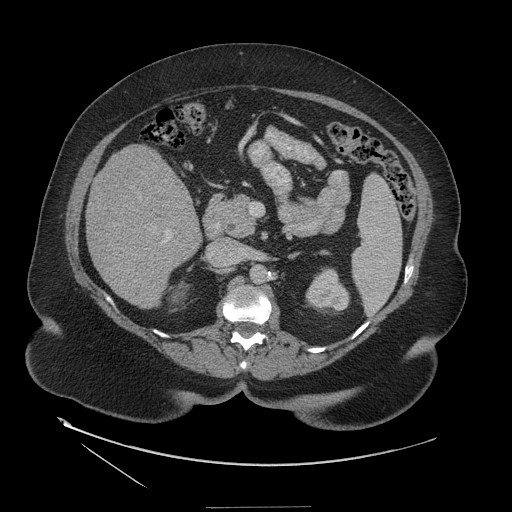
Contrast-enhanced abdominal CT (liver protocol), one axial slice; position 59 of 127 along the scan axis; reconstruction kernel STANDARD; soft-tissue window (W 400 / L 40 HU); 2.5 mm slice thickness; 512 × 512 image matrix, field of view 480 × 480 mm. Case-level facts recorded for this patient, not image findings: diagnosis: hepatocellular carcinoma (patient treated with transarterial chemoembolisation; whether this scan precedes or follows treatment is not stated here); TNM stage (as recorded): Stage-II; Child-Pugh class: A; tumour nodularity: multinodular; tumour size: 3 cm.
Annotated regions visible in this slice (semi-automatic segmentation, software-assisted and operator-edited):
- liver parenchyma outside the tumour (the mass and vessels are separate outlines, so this box may not span the whole liver): bounding box (x1, y1, x2, y2) in pixels: (86, 144, 200, 308)
- liver vessels: (164, 231, 169, 242)